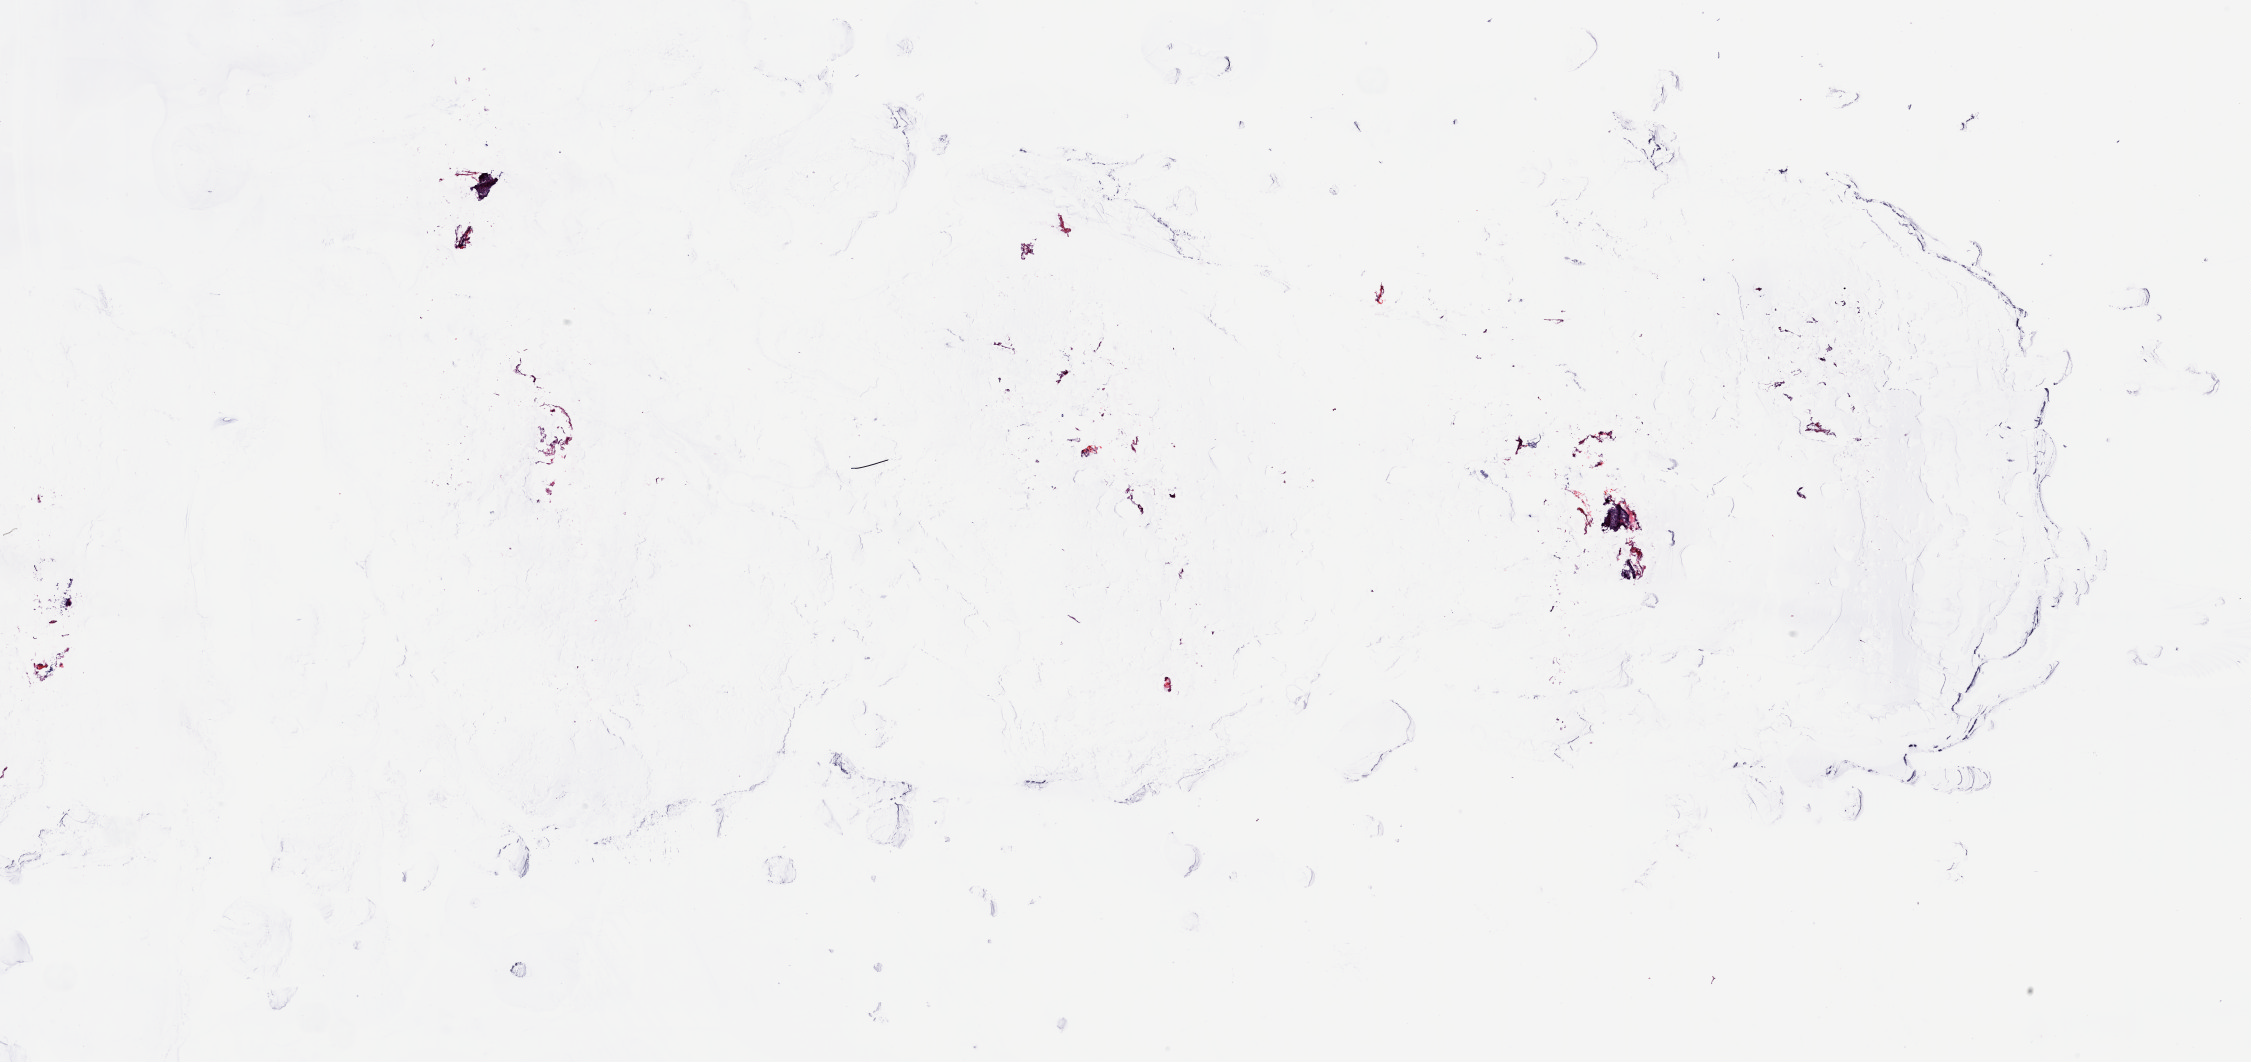
Whole-slide histology image, H&E — a low-resolution overview of the entire scanned area, about 35.7 x 16.8 mm, frozen section, thymus, solid tissue normal (non-tumour tissue) sample. Female, age 48 years at initial diagnosis. Slide review estimates, as recorded: tumour cells 0%, tumour nuclei 0%, normal cells 100%, stromal cells 0%, necrosis 0%. Inflammatory infiltration, as recorded: lymphocyte infiltration 0%, monocyte infiltration 0%, neutrophil infiltration 0%.
• this section: solid tissue normal sample (biorepository sample class)
• patient diagnosis: Thymoma, type B2, malignant